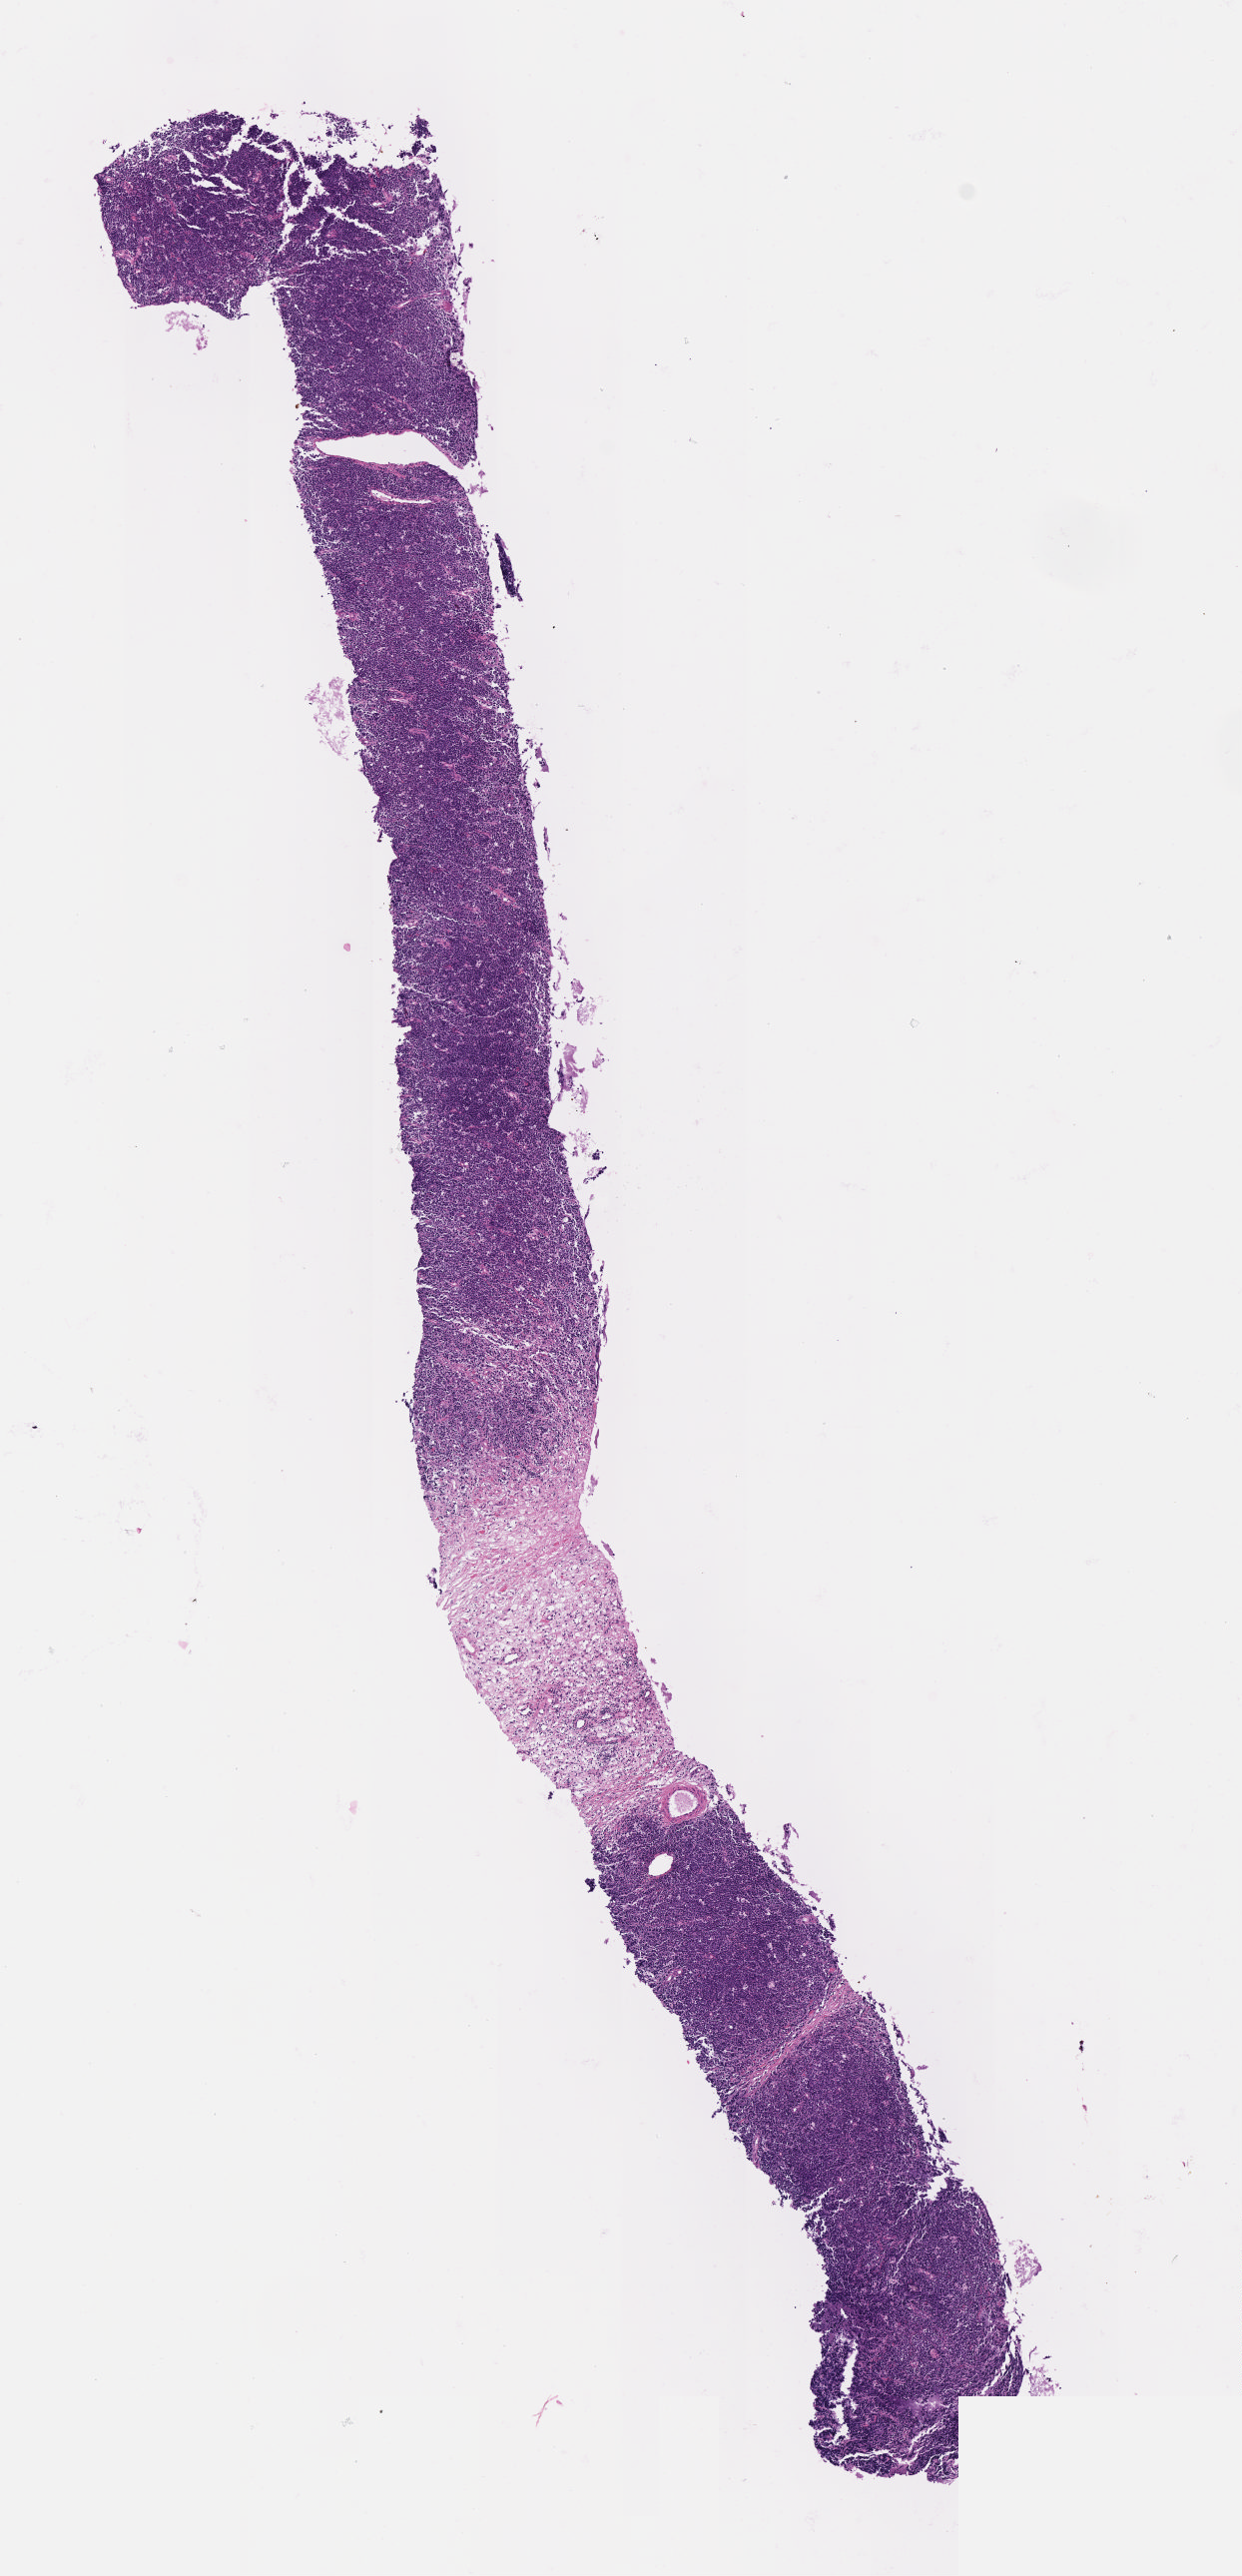
Hematoxylin and eosin (H&E) whole-slide image, shown as a low-resolution overview of the whole scanned area (about 5.0 x 10.4 mm), tumor tissue. Male patient; age at initial diagnosis 7 years.
Diagnosis: Neoplasm, uncertain whether benign or malignant.